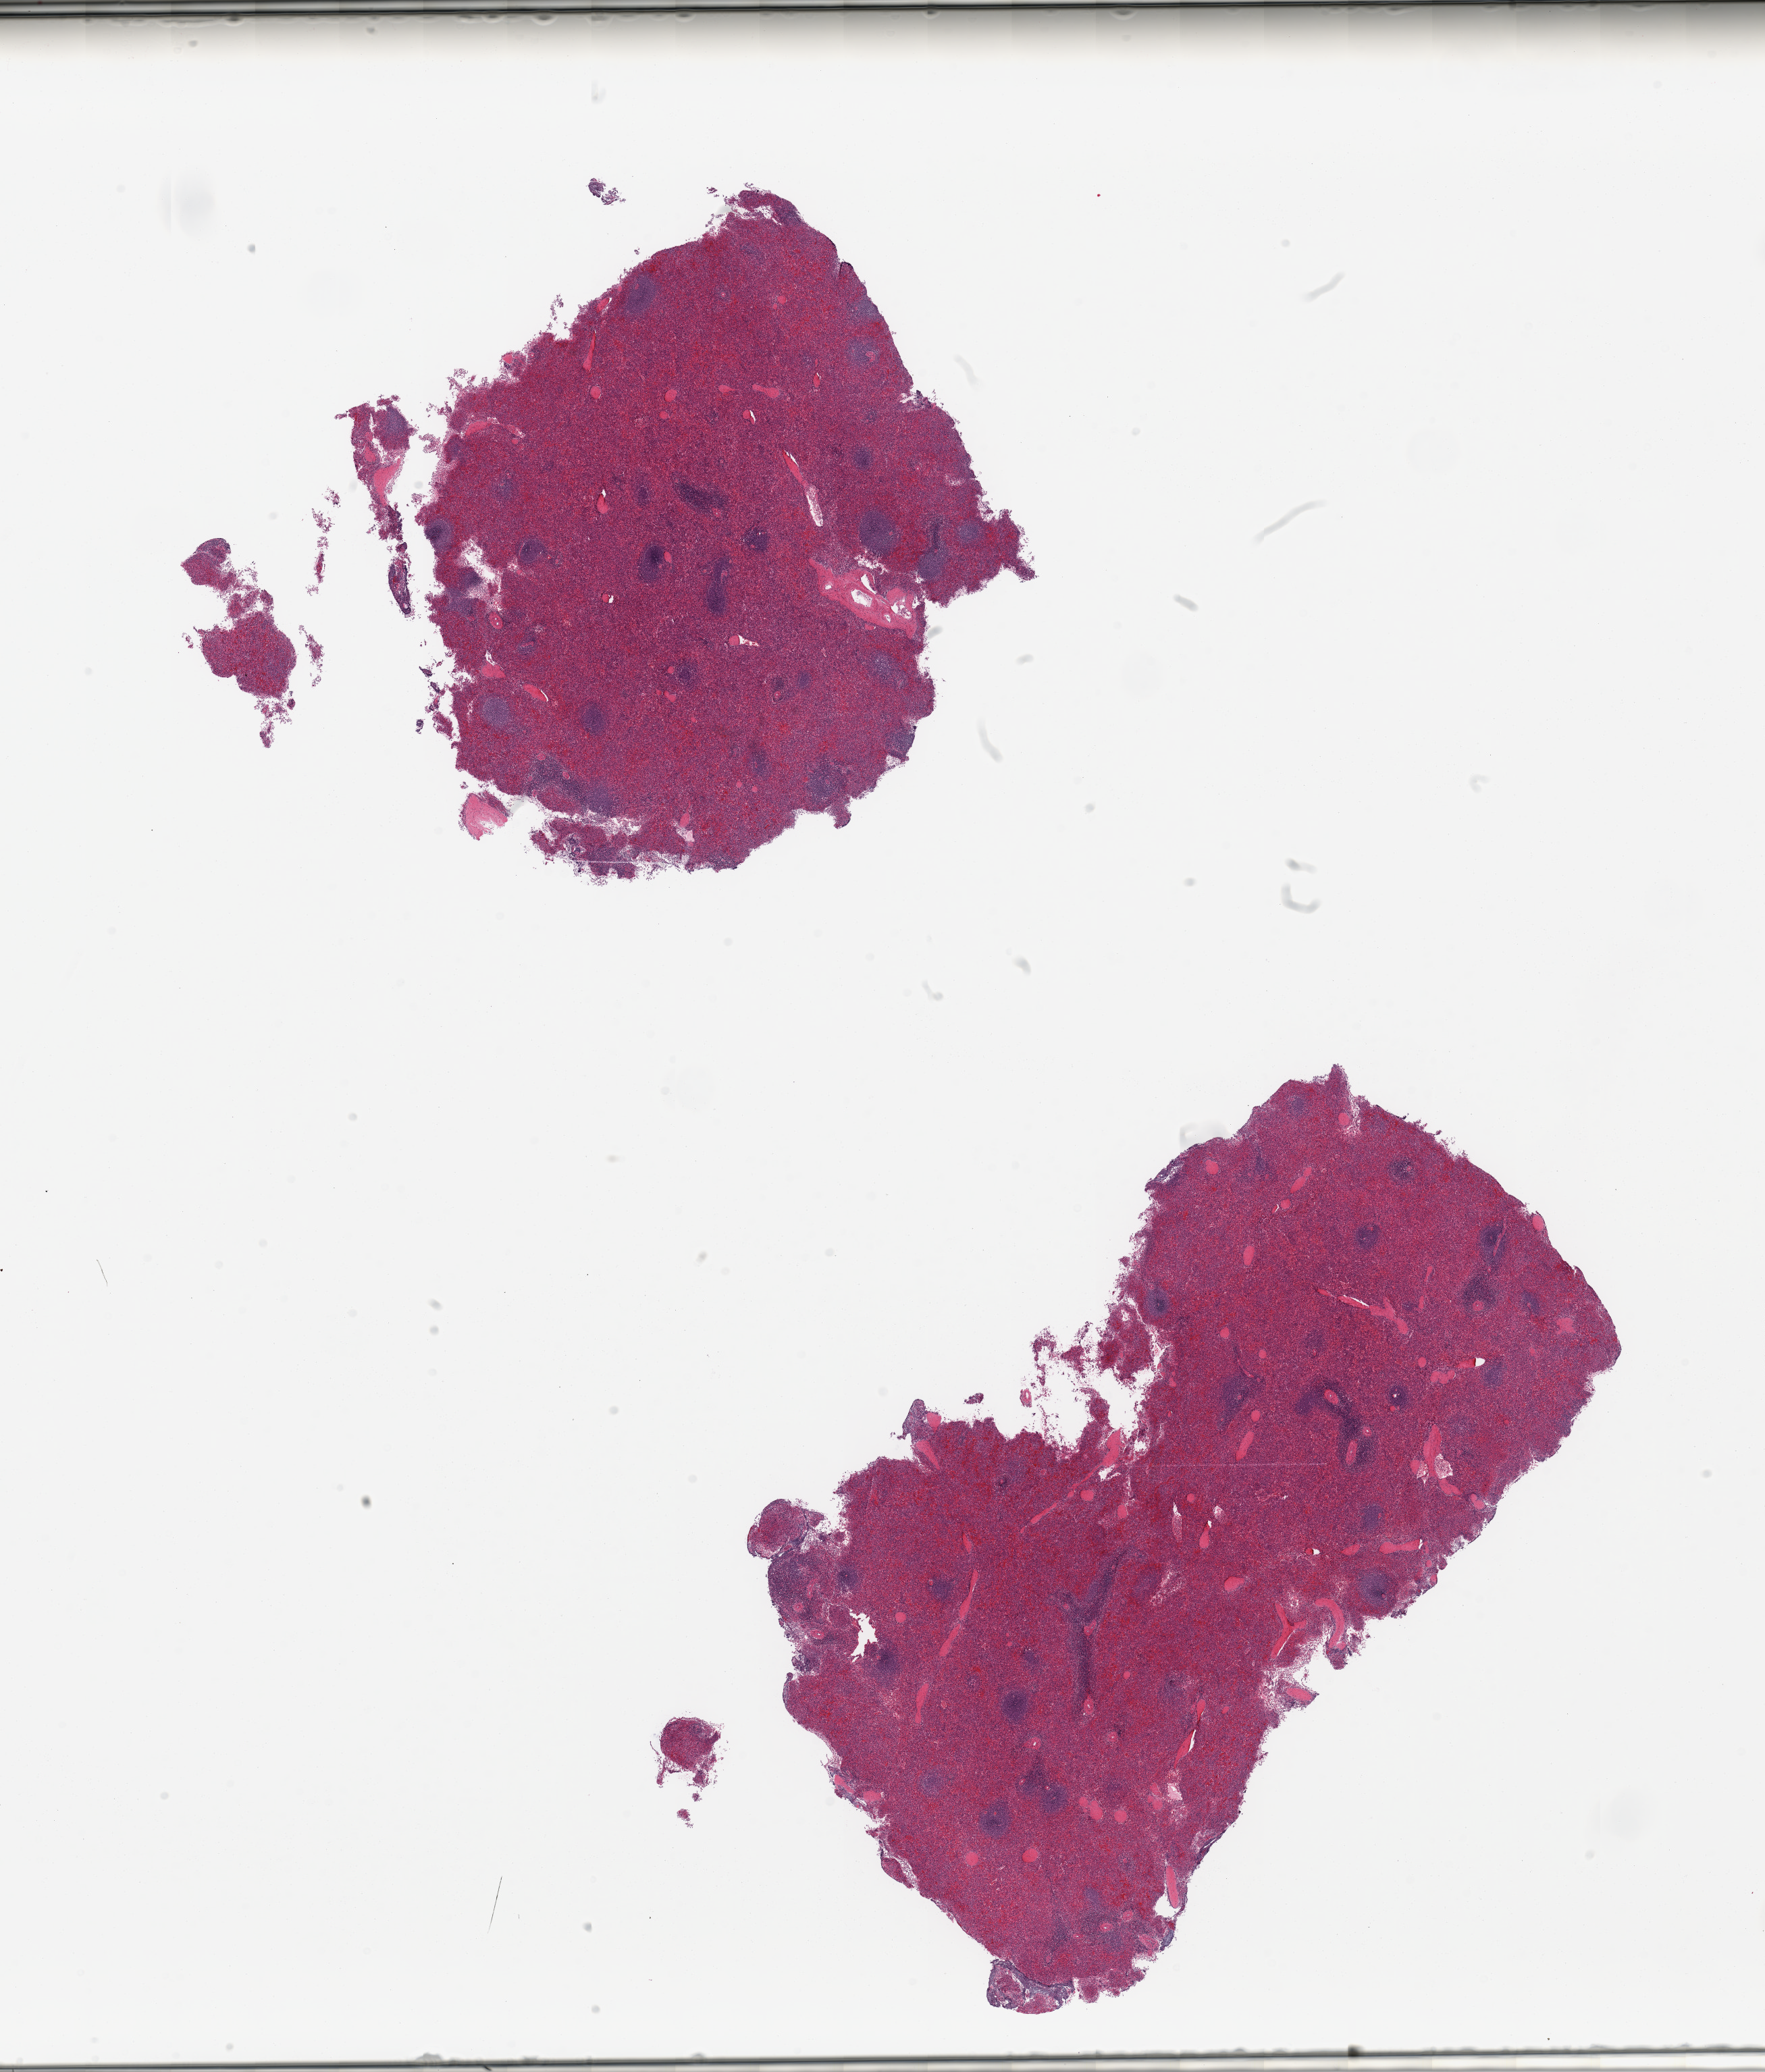
Whole-slide image, hematoxylin and eosin (H&E) stain, a low-resolution overview of the entire scanned area, about 20.7 x 24.3 mm (acquisition: 20x scan). PAXgene-fixed paraffin-embedded (PFPE) section. Sampled site (target tissue): spleen. Tissue donor sample. Male donor.
Review note (as recorded): 2 pieces; no abnormalities.